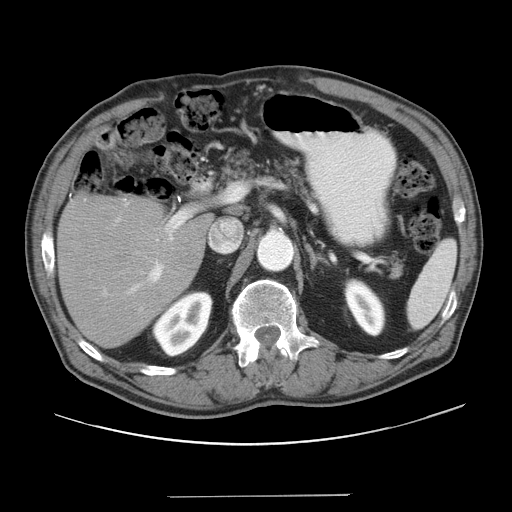
Contrast-enhanced abdominal CT, one axial slice; position 22 of 41 along the scan axis; reconstruction kernel STANDARD; intravenous contrast given; soft-tissue window (W 400 / L 40 HU); 512 × 512 image matrix, field of view 420 × 420 mm. Male patient, age 75 years. Case-level facts recorded for this patient, not image findings: diagnosis: colorectal cancer liver metastases, imaged before liver resection; multiple liver metastases: no.
Structures marked on this image (expert manual segmentation):
- liver: bounding box [x1, y1, x2, y2] px = [59, 194, 209, 347]
- planned liver remnant (the part of the liver to remain after resection): [59, 194, 210, 347]
- portal vein (with intrahepatic branches): [103, 200, 195, 296]